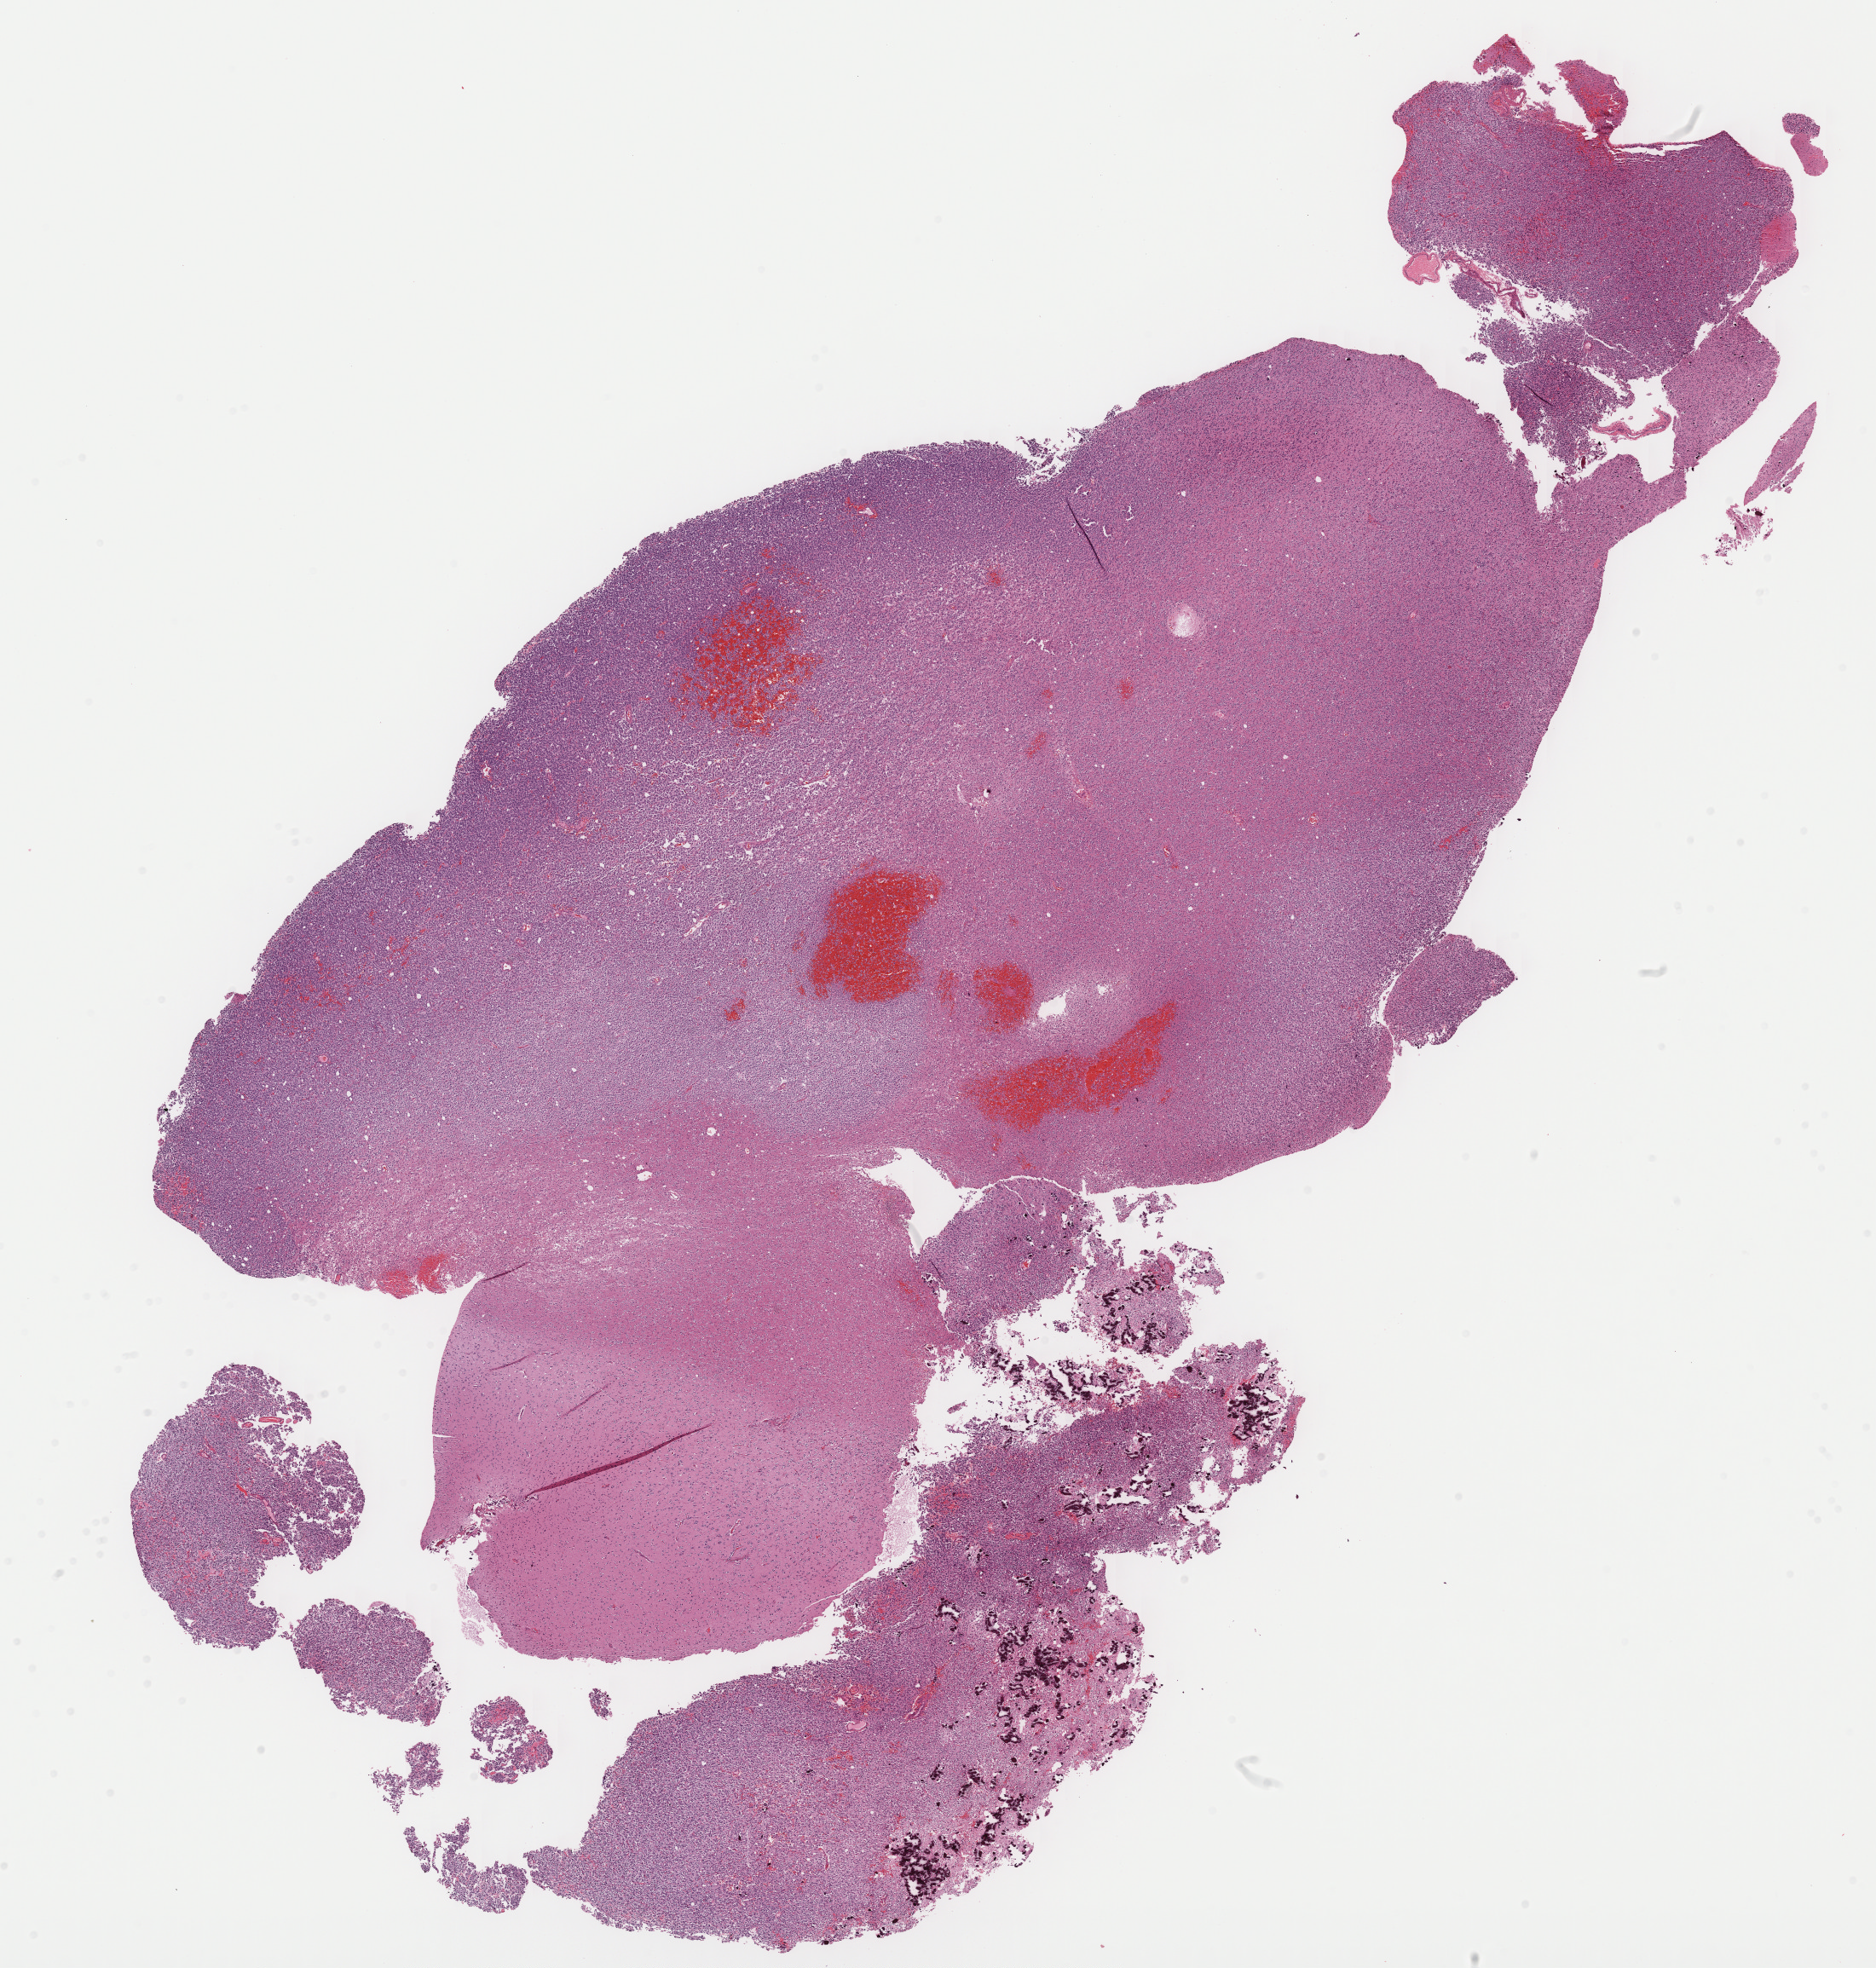
Digitized H&E tissue section (whole slide) — shown as a low-resolution overview of the whole scanned area (about 17.3 x 18.2 mm, acquisition: 40x scan); formalin-fixed paraffin-embedded (FFPE) diagnostic section; primary tumour sample from the brain. Patient: female, age at initial diagnosis 37 years. Histologic grade: G3 (poorly differentiated).
* diagnosis: Mixed glioma